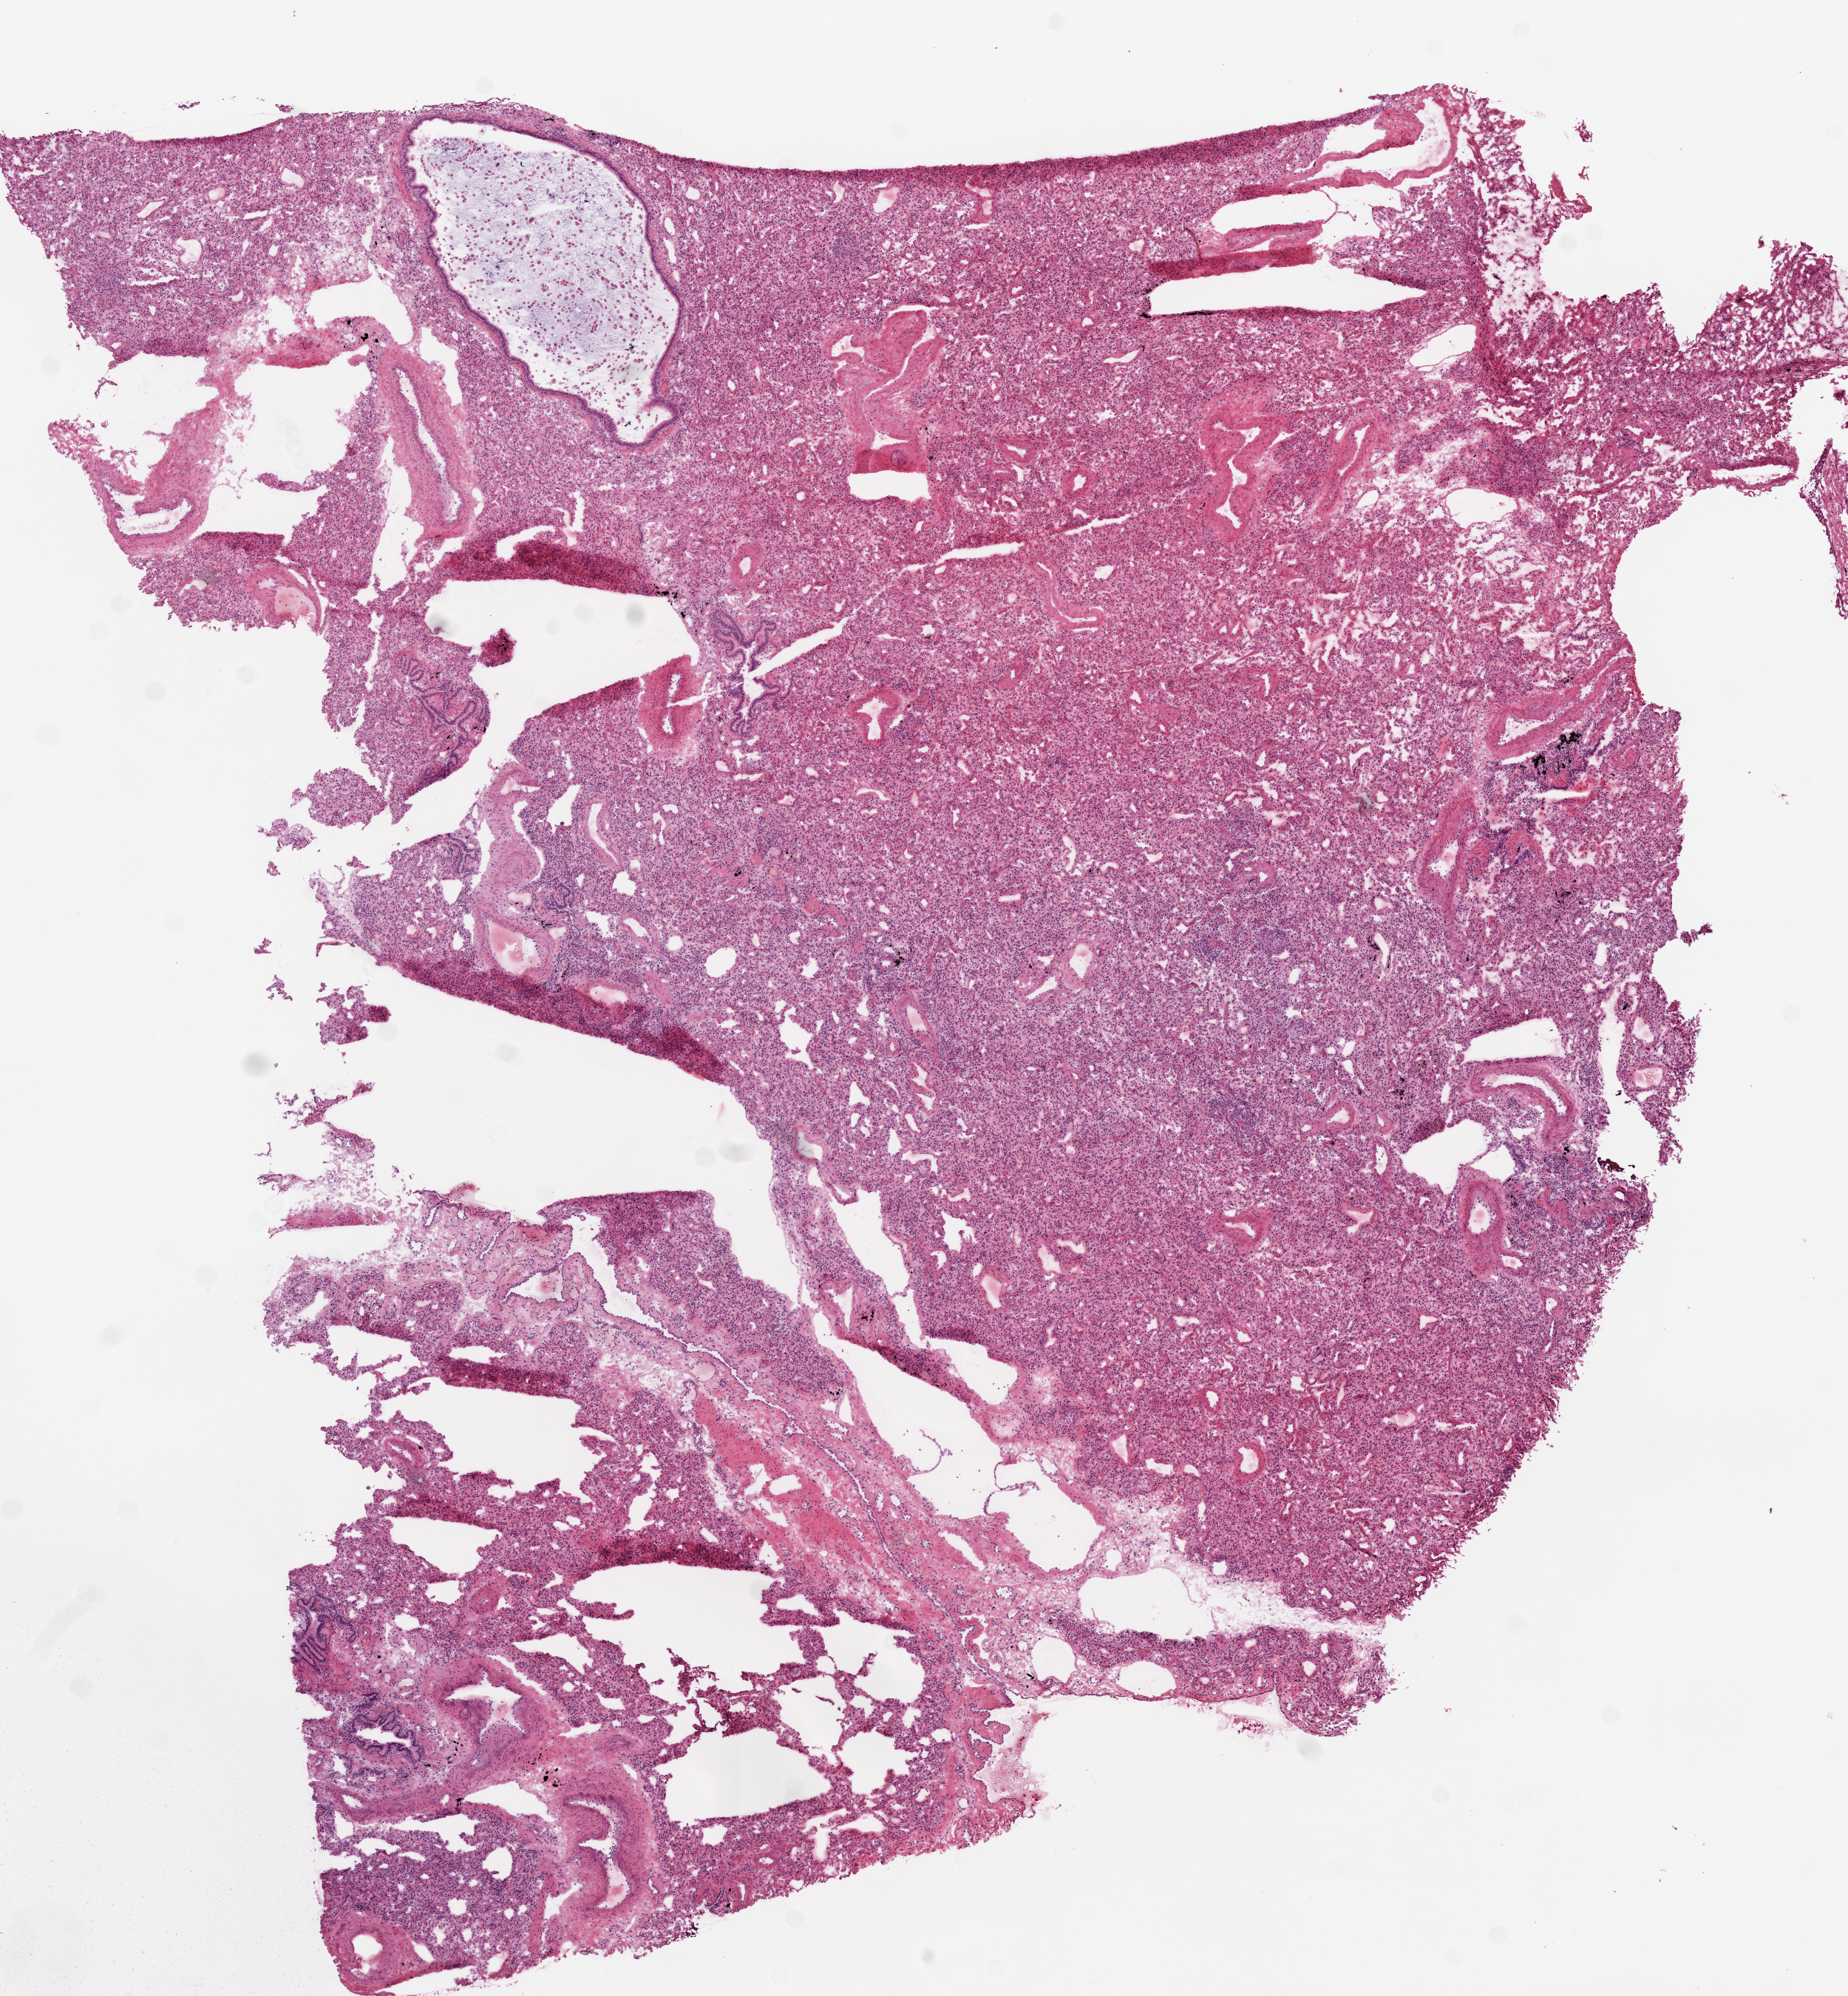
H&E whole-slide image — whole scanned area (about 10.0 x 10.8 mm, slide scanned at 20x) shown as a low-resolution overview; frozen section from the top of the tissue portion; sample: solid tissue normal (non-tumour tissue), lung. Patient: male, age at initial diagnosis 68 years.
This section: solid tissue normal sample (biorepository sample class). Patient diagnosis: Squamous cell carcinoma, NOS.